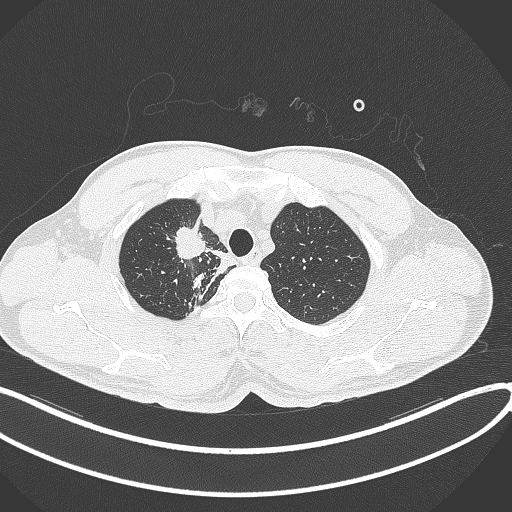
Chest CT, one axial slice. Slice 322 of 391 in the series (ordered by position). Reconstruction kernel B70f. 120 kVp. Lung window (W 1500 / L -600 HU). 1 mm slice thickness. 512 × 512 image matrix. Patient: male, 48 years. From the clinical record (not read from this slice): clinical TNM (as recorded): T1c N1 M1.
Annotated regions visible in this slice (rectangle marked by the reading radiologist):
- lung tumour (recorded histology: adenocarcinoma): bounding box <169,221,208,261> (left, top, right, bottom; pixels)